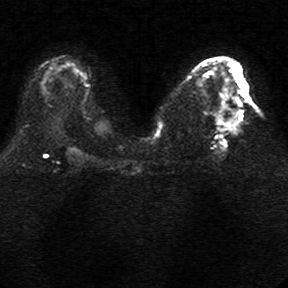
Breast MRI, one axial slice; position 15 of 34 along the scan axis; diffusion-weighted series; image 2 of 4 stored at this slice position (different b-values; order by instance number); 1.5 T; 288 × 288 image matrix. Female patient.
Structures marked on this image (manually delineated by an expert):
- tumour on diffusion-weighted imaging: bounding box <228,97,239,123> (left, top, right, bottom; pixels)